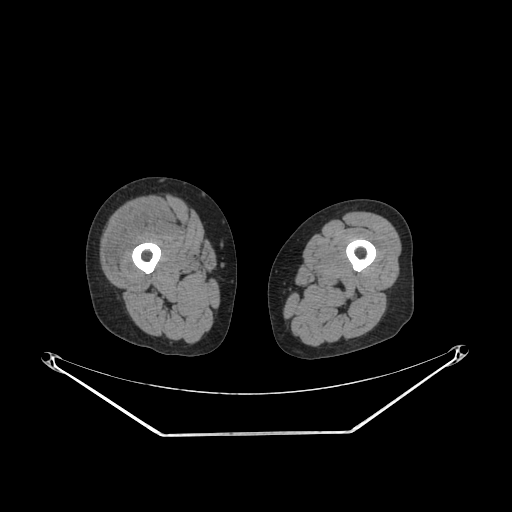
CT of an extremity soft-tissue mass (from a PET/CT study), one axial slice. Position 224 of 311 along the scan axis. Reconstruction kernel SOFT. 140 kVp. Soft-tissue window (W 400 / L 40 HU). 3.75 mm slice thickness. 512 × 512 image matrix. Female patient. From the clinical record (not read from this slice): histological type: pleiomorphic undifferentiated sarcoma; grade: high; site of the primary tumour: right quadricep.
Outlined on this slice (expert contour drawn on MRI and transferred to this co-registered scan by the dataset authors):
- tumour plus oedema (research contour): box from (x=107, y=208) to (x=165, y=273) px